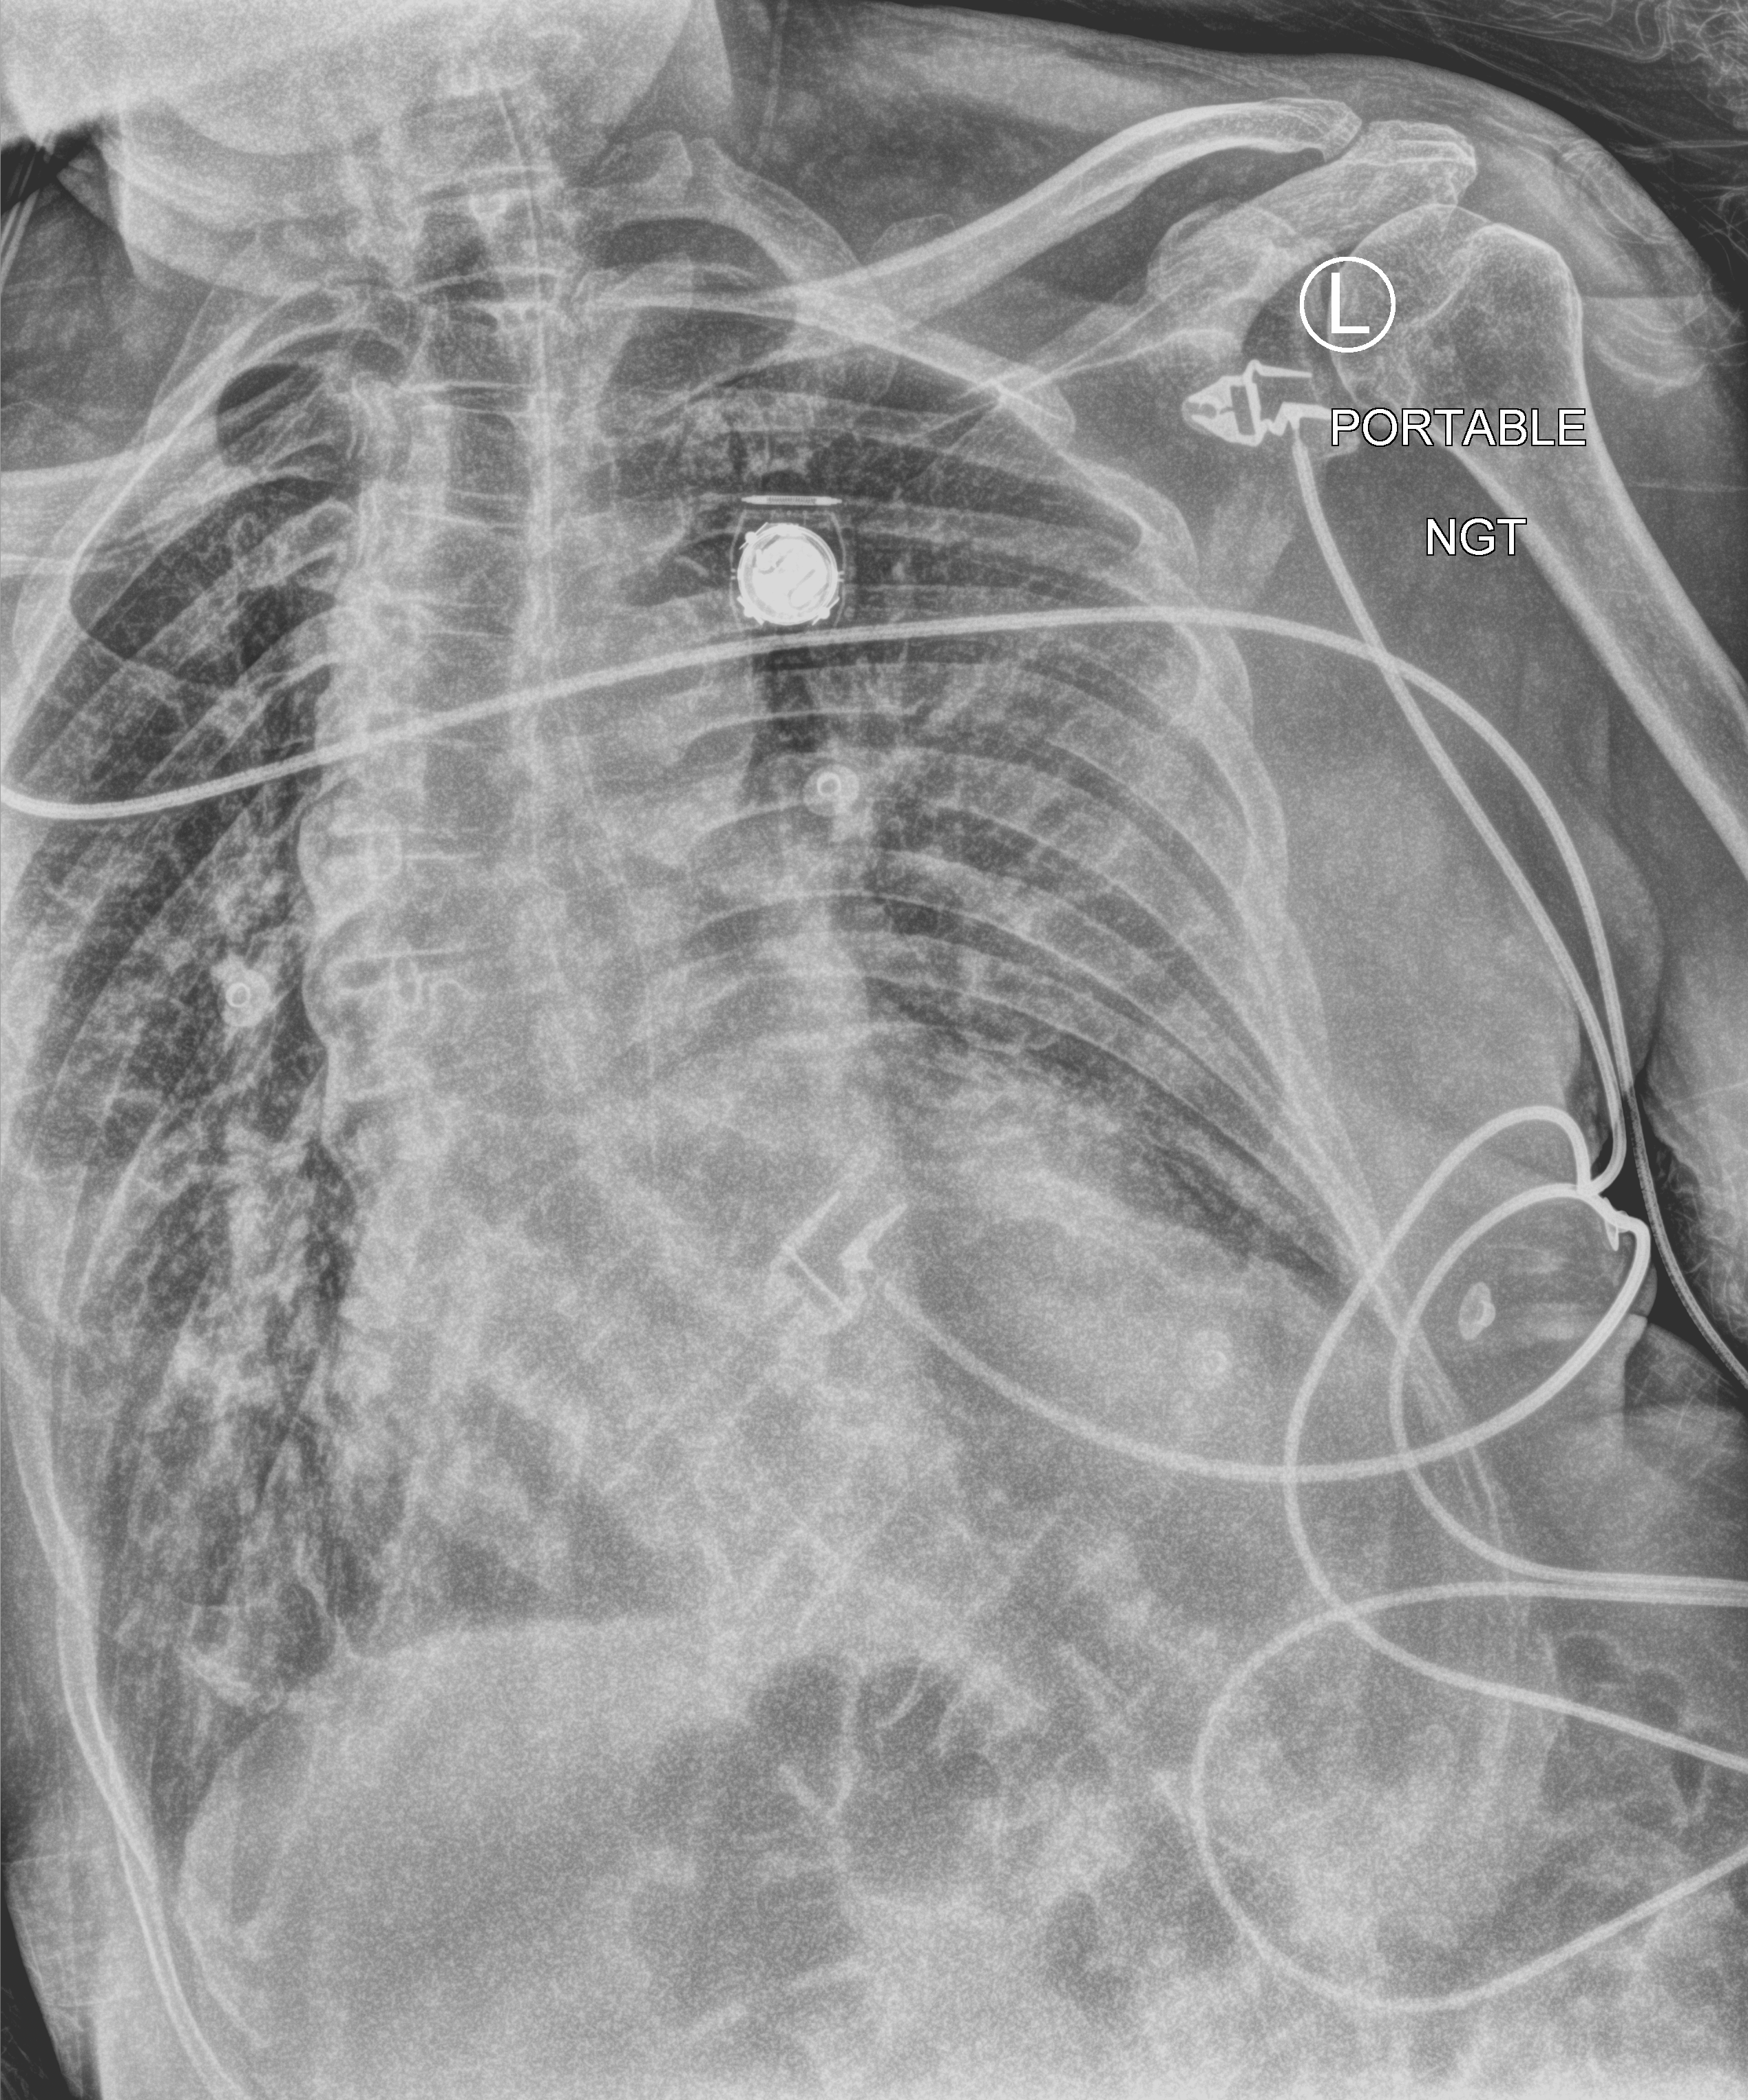
Portable chest radiograph; anteroposterior (AP) projection. Male patient hospitalised with COVID-19, age 75–90 years.
Admission-level facts for this patient (not findings on this image; timing relative to this image not recorded): admitted to intensive care during this hospital stay: no.